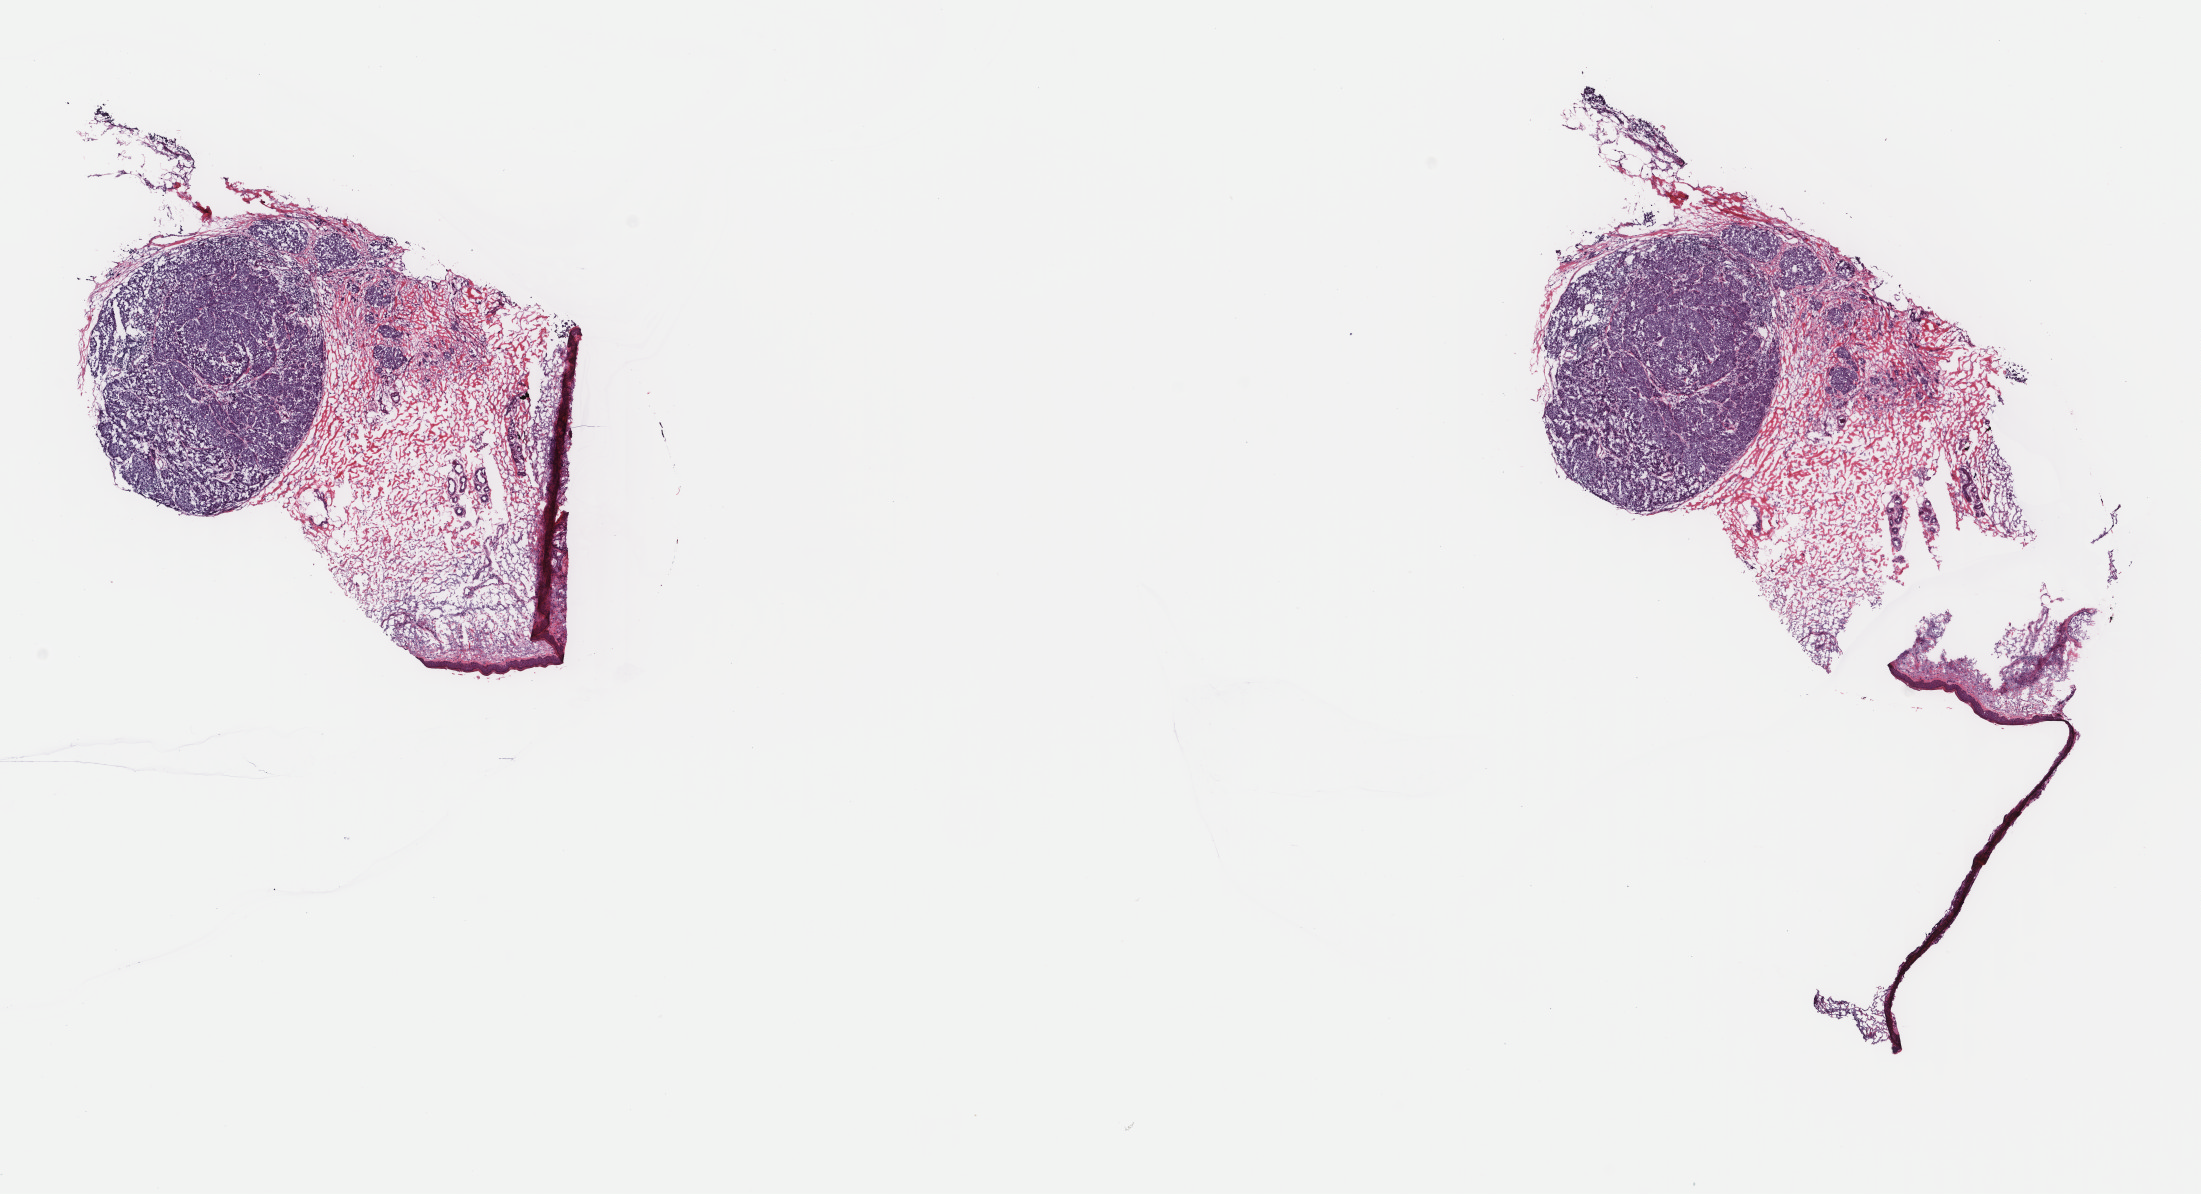
Digitized H&E tissue section (whole slide), shown as a low-resolution overview of the whole scanned area (about 17.5 x 9.5 mm, slide scanned at 40x), frozen section, metastatic tumour sample, sampled site: connective, subcutaneous and other soft tissues of upper limb and shoulder. Male patient; age at initial diagnosis 78 years. Composition of this section per pathologist review: tumour cells 75%, tumour nuclei 75%, normal cells 5%, stromal cells 19%, necrosis 1%. Inflammatory infiltration, as recorded: lymphocyte infiltration 4%, monocyte infiltration 1%, neutrophil infiltration 0%.
* this section: metastatic tumour tissue
* patient diagnosis: Malignant melanoma, NOS